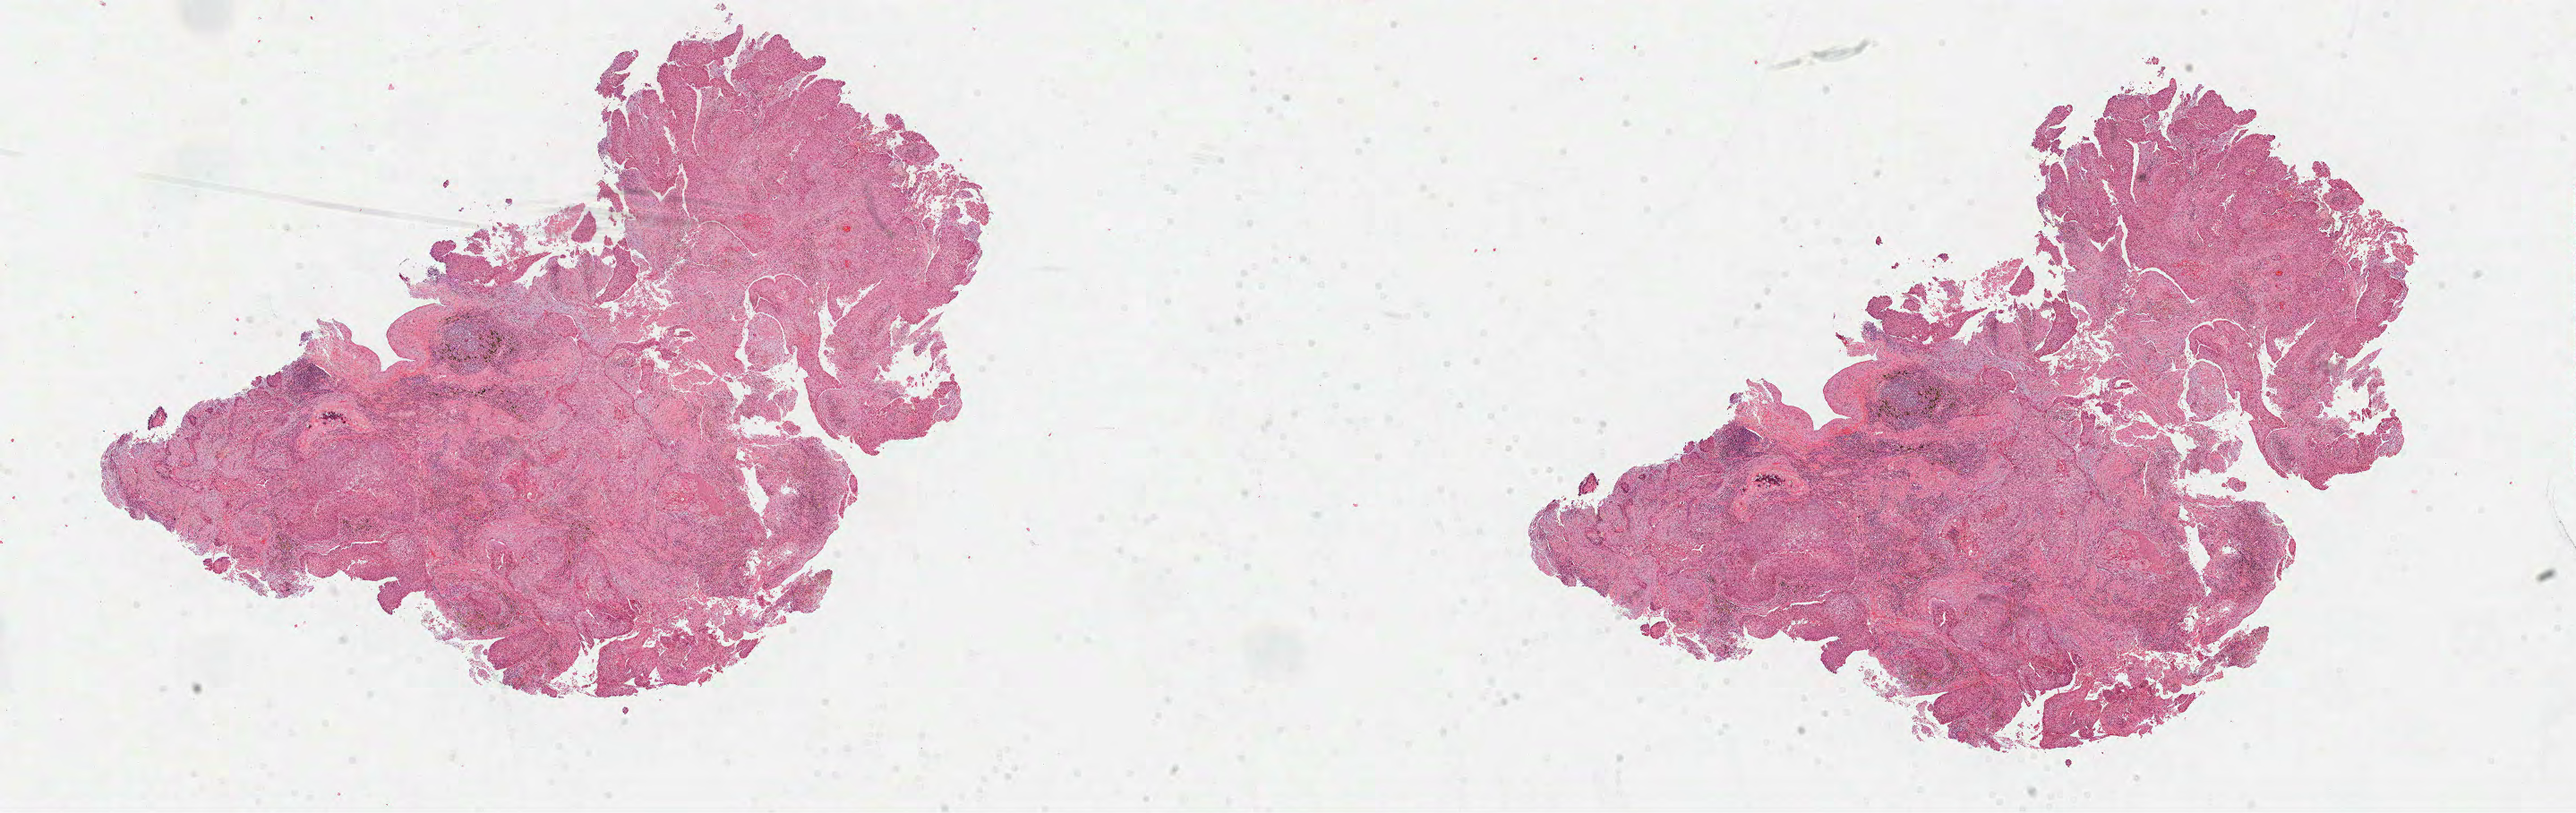
H&E whole-slide image — a low-resolution overview of the entire scanned area, about 23.2 x 7.3 mm (slide scanned at 40x); formalin-fixed paraffin-embedded (FFPE) diagnostic section; primary tumour sample from the lung. Female patient; age at initial diagnosis 75 years.
Diagnosis: Squamous cell carcinoma, NOS (upper lobe, lung).